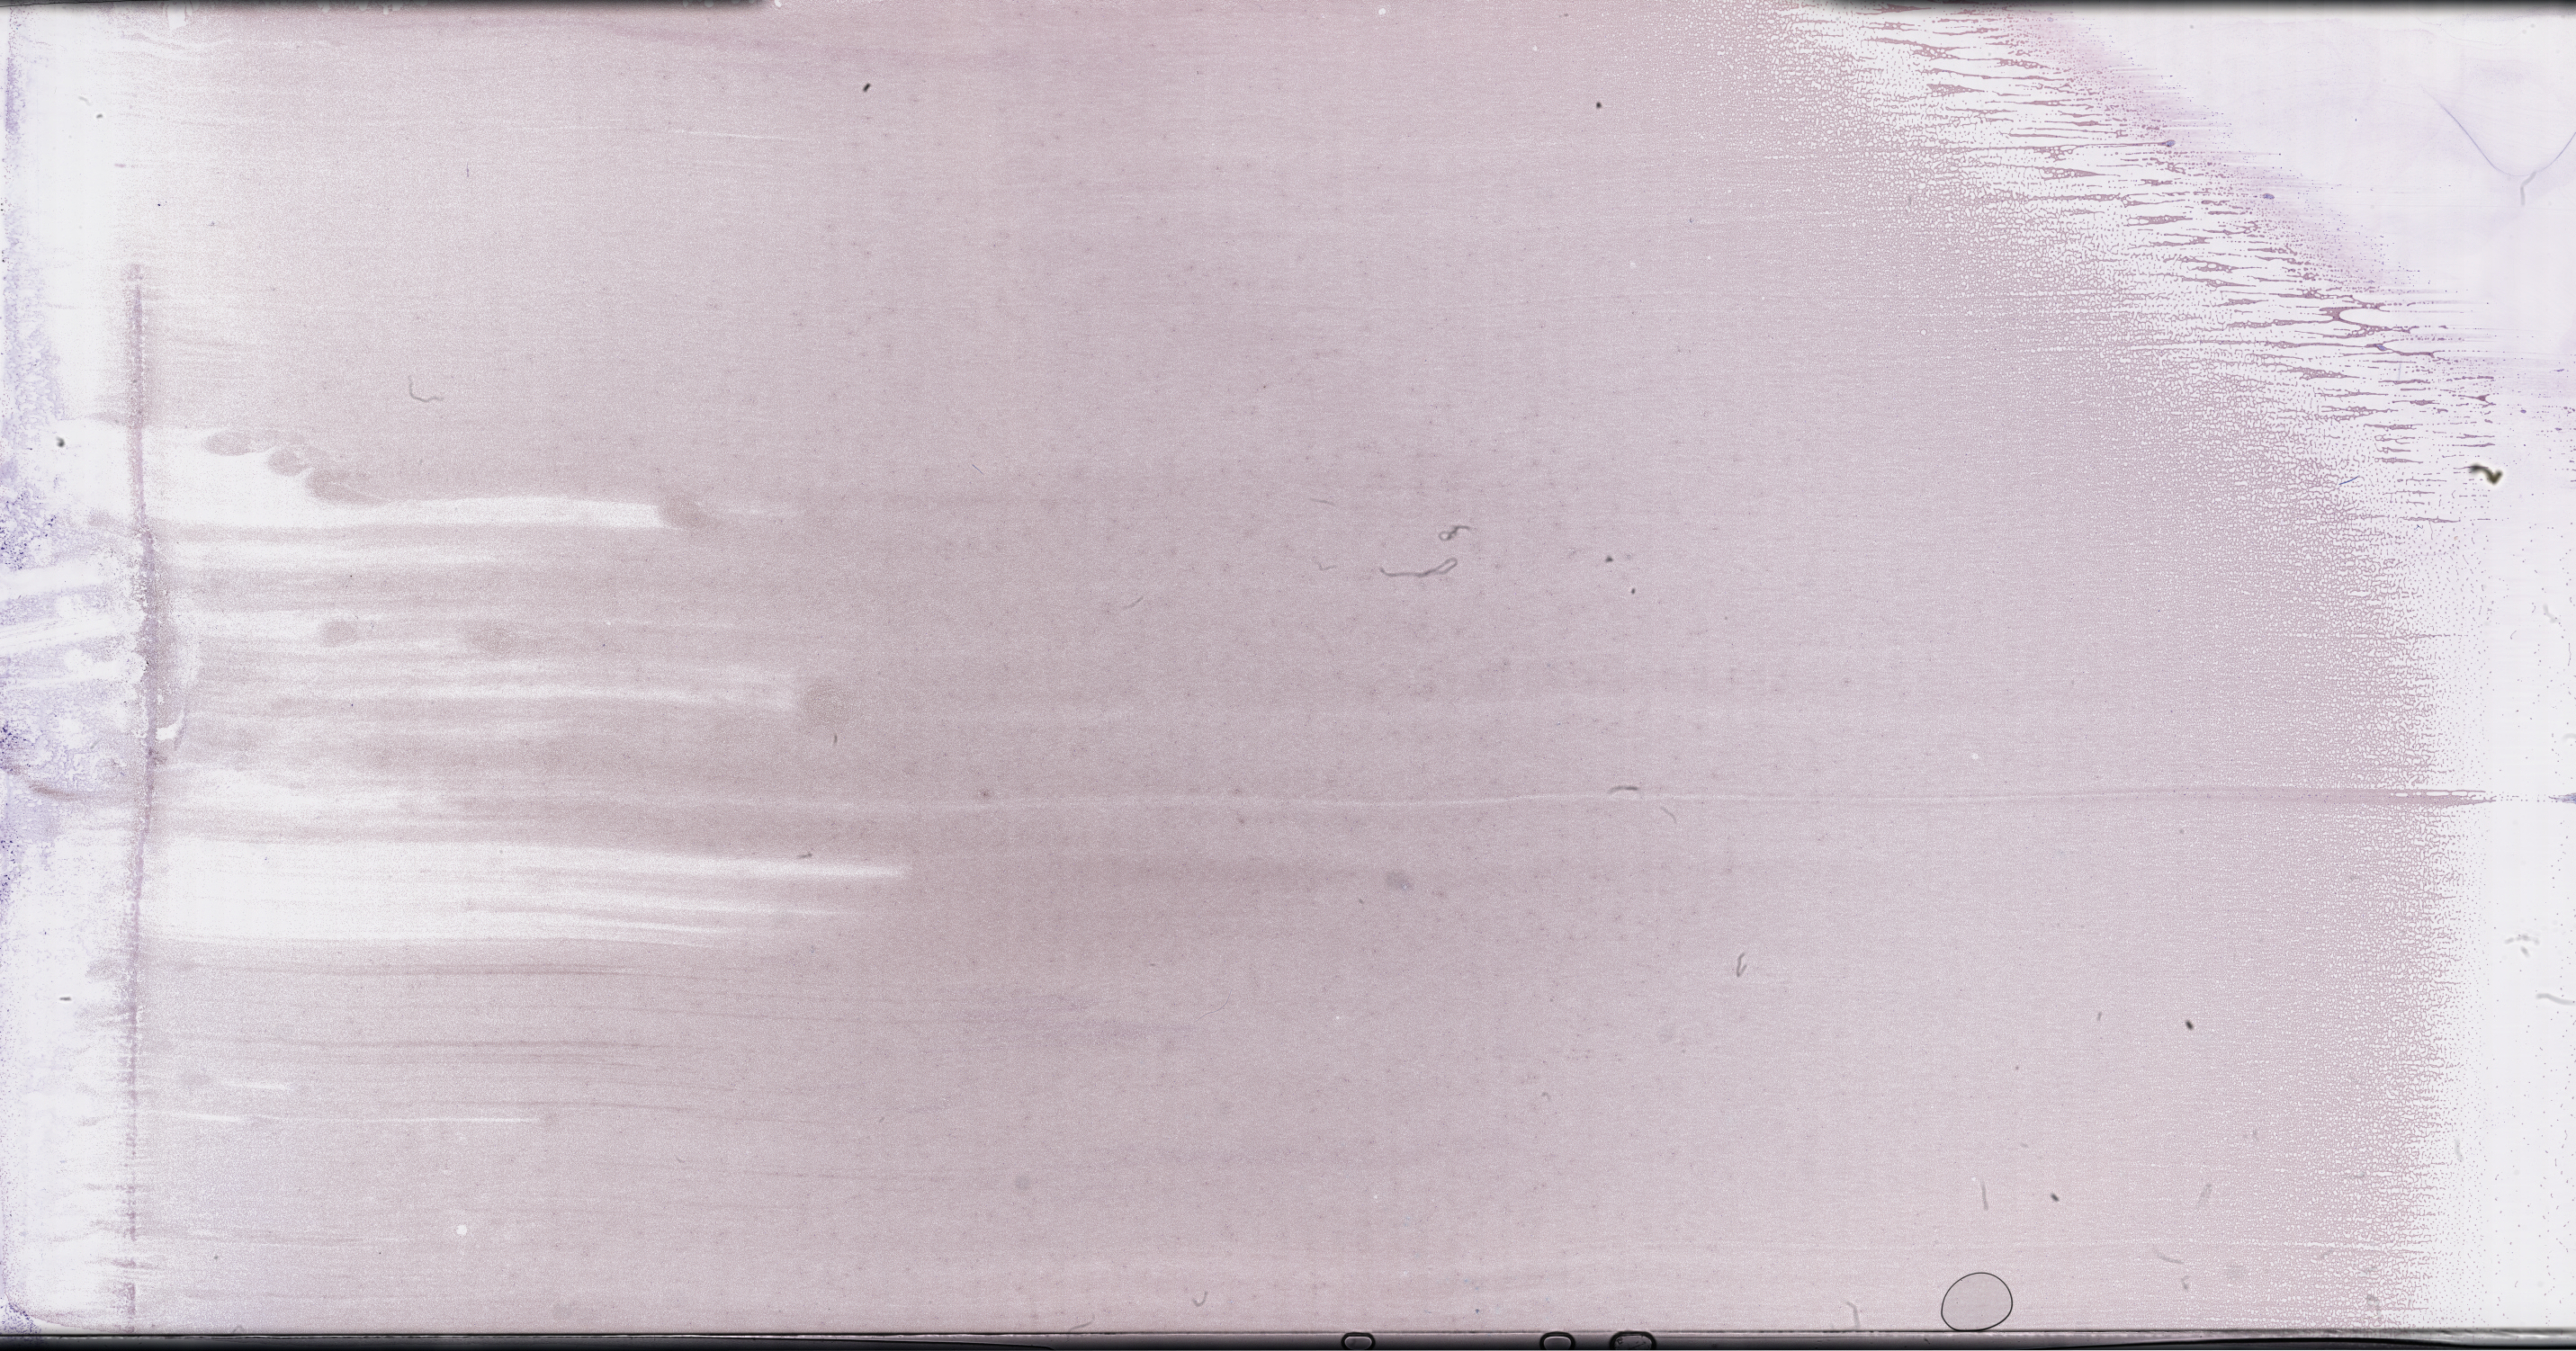
Whole-slide image of a whole blood smear, Wright-Giemsa stain — a low-resolution overview of the entire scanned area, about 46.2 x 24.3 mm. Collected on treatment. Female patient.
Patient diagnosis: Plasma Cell Myeloma.